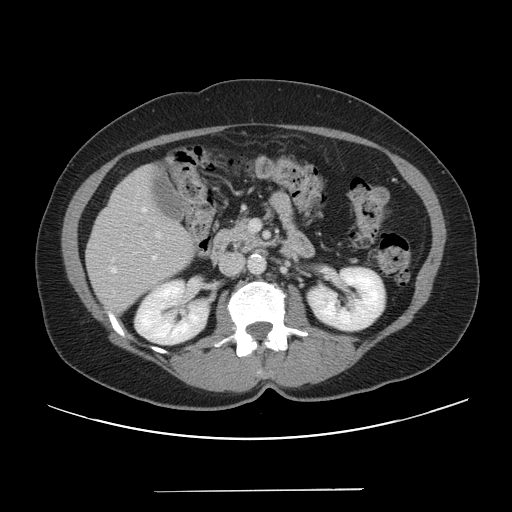
Contrast-enhanced abdominal CT, one axial slice; position 19 of 56 along the scan axis; intravenous contrast given; soft-tissue window (W 400 / L 40 HU); 512 × 512 image matrix. Female patient, age 54 years. From the clinical record (not read from this slice): diagnosis: colorectal cancer liver metastases, imaged before liver resection; multiple liver metastases: yes; largest metastasis: 3.2 cm.
Outlined on this slice (outlined manually by an expert reader):
- hepatic veins: bounding box [x1, y1, x2, y2] px = [112, 268, 116, 272]
- liver: [87, 166, 193, 315]
- portal vein (with intrahepatic branches): [157, 221, 259, 237]